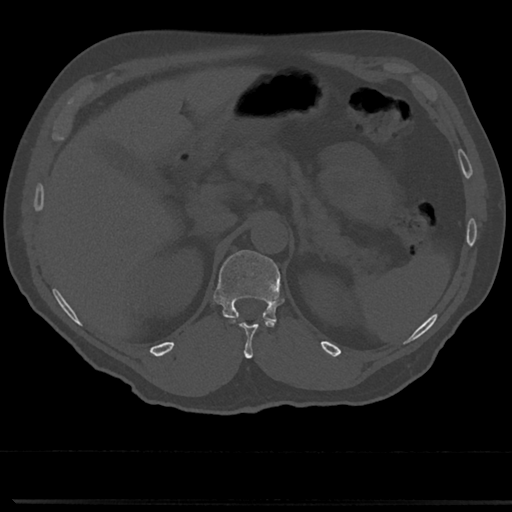
CT including the spine, one axial slice. Position 168 of 817 along the scan axis. Reconstruction kernel Br40s/3. 120 kVp. Bone window (W 1800 / L 400 HU). 0.5 mm slice thickness. 512 × 512 image matrix, field of view 355 × 355 mm. Male patient, age 61 years. From the clinical record (not read from this slice): primary cancer: prostate.
Outlined on this slice (semi-automatically segmented with operator editing):
- T11 vertebra: bounding box <232,327,253,358> (left, top, right, bottom; pixels)
- T12 vertebra: <214,250,286,337>